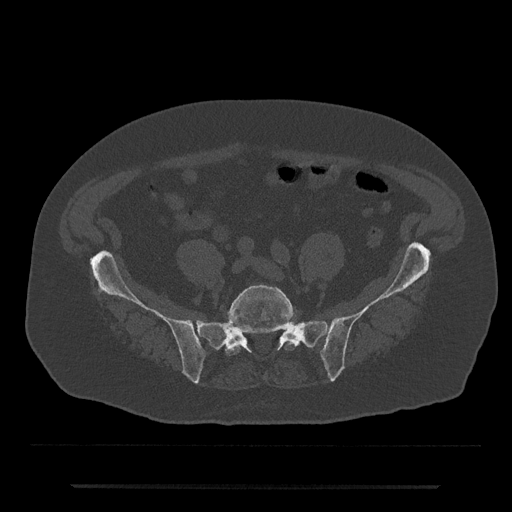
CT including the spine, one axial slice; slice 260 of 797 in the series (ordered by position); reconstruction kernel Br40s/3; bone window (W 1800 / L 400 HU); 0.5 mm slice thickness; 512 × 512 image matrix, field of view 434 × 434 mm. Male patient, age 80 years. Case-level facts recorded for this patient, not image findings: primary cancer: prostate; vertebrae with lytic lesions (as recorded): L1, T11.
Structures marked on this image (semi-automatic segmentation, software-assisted and operator-edited):
- L5 vertebra: box from (x=225, y=284) to (x=295, y=356) px